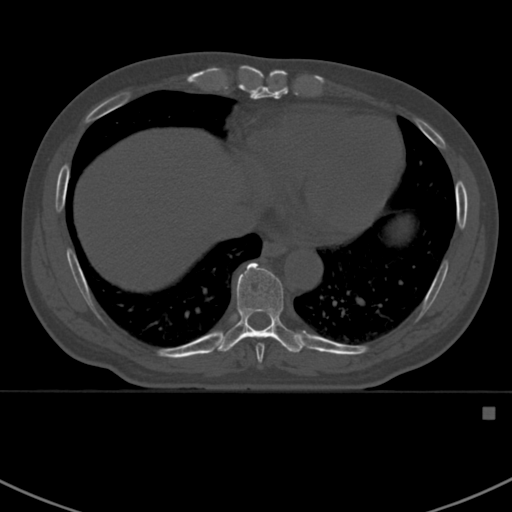
CT including the spine, one axial slice. Position 387 of 412 along the scan axis. Bone window (W 1800 / L 400 HU). 1.5 mm slice thickness. 512 × 512 image matrix, field of view 358 × 358 mm. Patient: male, 59 years. From the clinical record (not read from this slice): primary cancer: prostate.
Outlined on this slice (semi-automatic segmentation, software-assisted and operator-edited):
- T8 vertebra: bounding box <256,344,264,369> (left, top, right, bottom; pixels)
- T9 vertebra: <216,262,305,353>